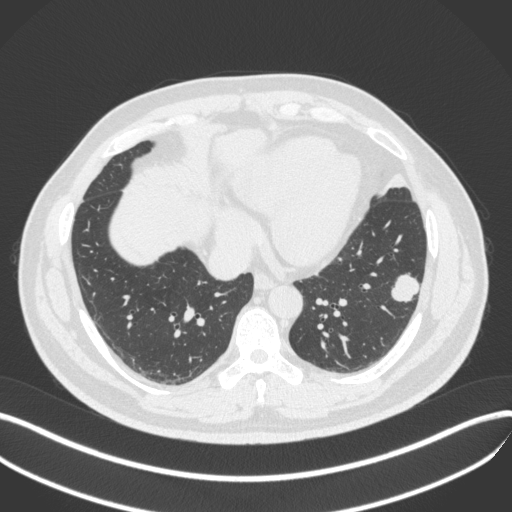
Chest CT, one axial slice; position 144 of 420 along the scan axis; 120 kVp; lung window (W 1500 / L -600 HU); 512 × 512 image matrix, field of view 400 × 400 mm. Male patient, age 39 years. Case-level facts recorded for this patient, not image findings: clinical TNM (as recorded): T2a N0 M0.
Annotated regions visible in this slice (bounding box drawn by a radiologist):
- lung tumour (recorded histology: adenocarcinoma): bounding box <384,265,421,310> (left, top, right, bottom; pixels)